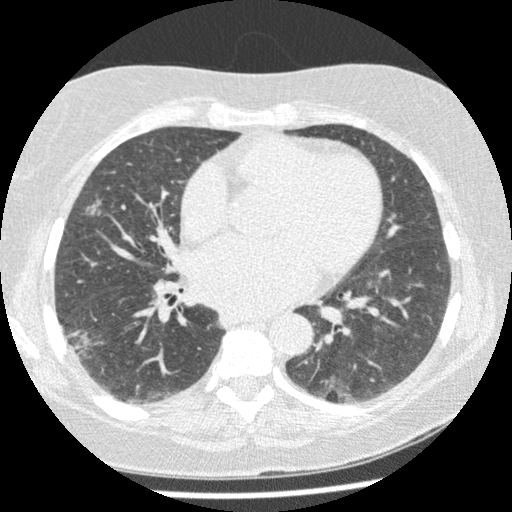
Low-dose screening chest CT, one axial slice. Position 115 of 241 along the scan axis. Reconstruction kernel STANDARD. Lung window (W 1500 / L -600 HU). 512 × 512 image matrix.
Outlined on this slice (expert manual segmentation):
- lesion 1 (tumor, lower lobe of right lung): box from (x=67, y=330) to (x=93, y=359) px